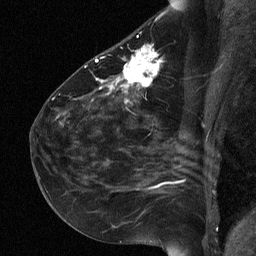
Breast MRI (dynamic contrast-enhanced), one sagittal slice. Dynamic contrast-enhanced study with each time point stored as its own series, time point 2 of 3 at this slice position (early post-contrast, ordered by acquisition time). 1.5 T. TE 4.8 ms, TR 27 ms. 2 mm slice thickness. 256 × 256 image matrix, field of view 180 × 180 mm. Patient: female, 51 years. From the clinical record (not read from this slice): setting: breast cancer imaged before/during neoadjuvant chemotherapy; receptor status: HR-positive, HER2-negative.
Outlined on this slice (semi-automatically segmented with operator editing):
- analysis volume of interest (the breast-tissue region the enhancement analysis was run in; not a lesion): bounding box (x1, y1, x2, y2) in pixels: (72, 34, 163, 118)
- tumour enhancement mask (voxels above the 90 % enhancement threshold inside the analysis volume of interest): (96, 46, 160, 103)